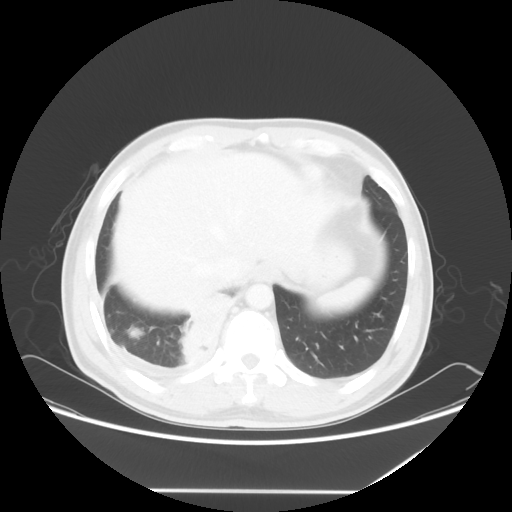
Chest CT, one axial slice. Position 14 of 60 along the scan axis. Reconstruction kernel STANDARD. Lung window (W 1500 / L -600 HU). 512 × 512 image matrix. Patient: male, 48 years. Case-level facts recorded for this patient, not image findings: clinical TNM (as recorded): T3 N3 M1a.
Outlined on this slice (rectangle marked by the reading radiologist):
- lung tumour (recorded histology: squamous cell carcinoma): box from (x=174, y=286) to (x=235, y=367) px